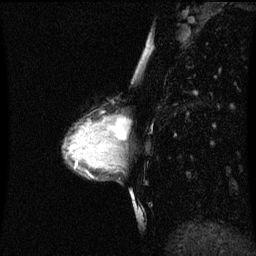
Breast MRI (dynamic contrast-enhanced), one sagittal slice. Dynamic contrast-enhanced series, image 2 of 3 at this slice position (ordered by acquisition). 1.5 T. TE 4.2 ms, TR 8.9 ms. 256 × 256 image matrix, field of view 200 × 200 mm. Female patient, age 33 years. From the clinical record (not read from this slice): setting: breast cancer imaged before/during neoadjuvant chemotherapy; receptor status: HER2-positive.
Structures marked on this image (semi-automatically segmented with operator editing):
- analysis volume of interest (the breast-tissue region the enhancement analysis was run in; not a lesion): bounding box <107,110,124,147> (left, top, right, bottom; pixels)
- tumour enhancement mask (voxels above the 70 % enhancement threshold inside the analysis volume of interest): <112,116,123,141>